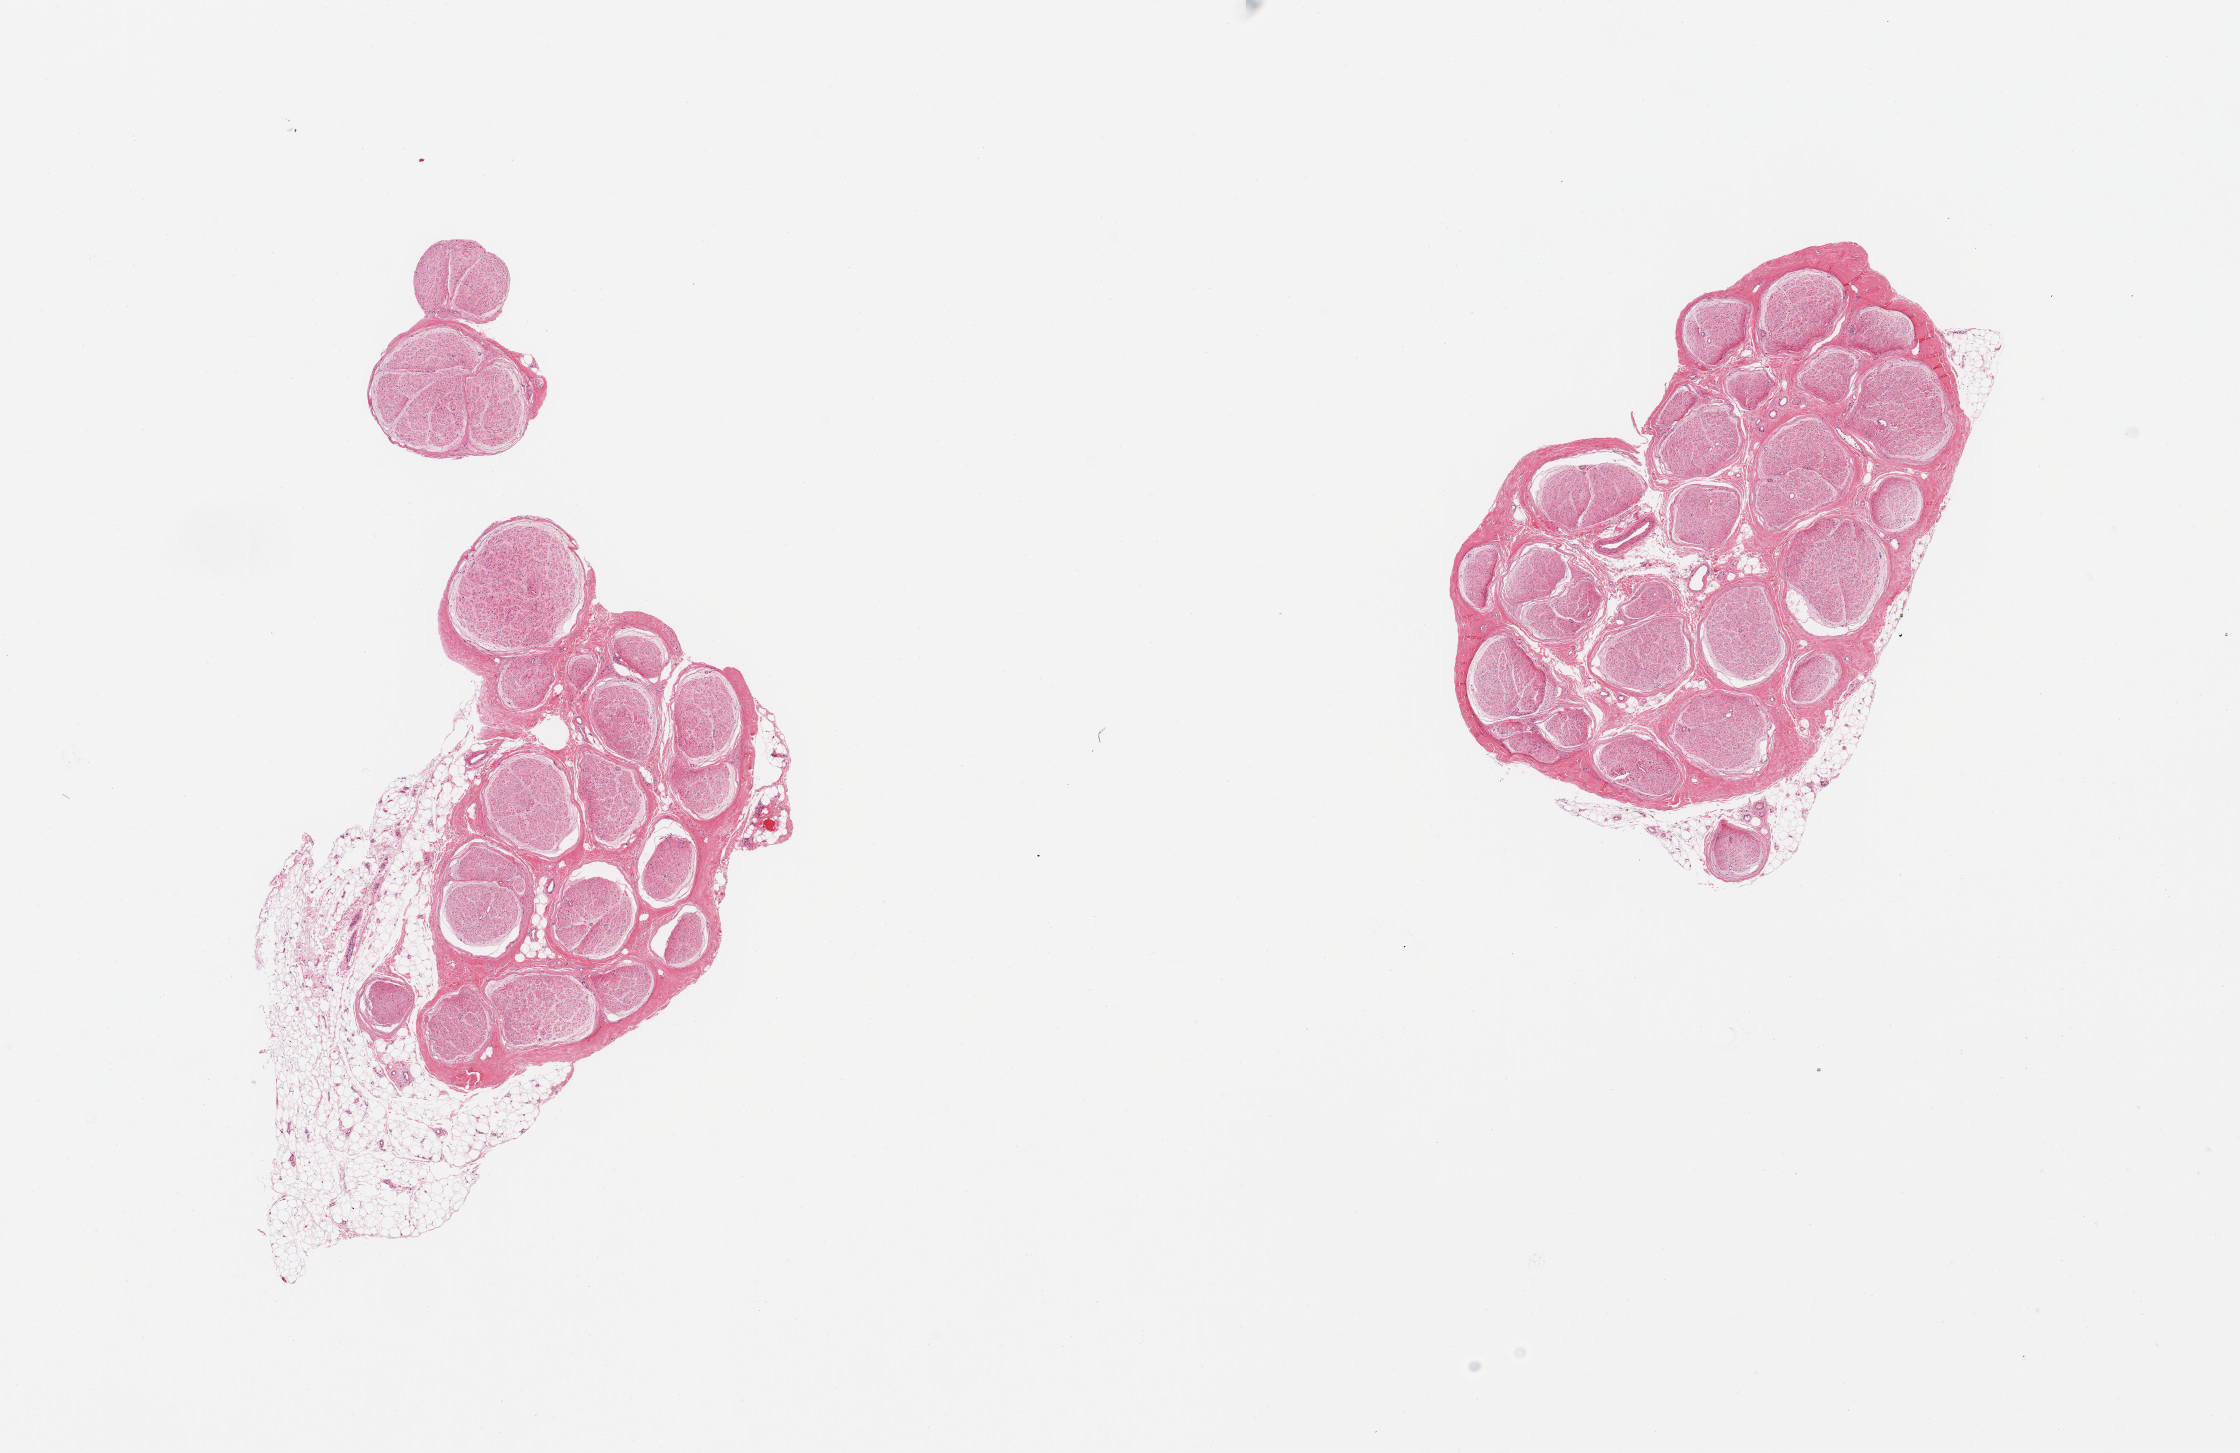
Digitized hematoxylin and eosin (H&E)-stained section, brightfield, low-resolution overview of the scanned area, about 17.7 x 11.5 mm (acquisition: 20x scan). PAXgene-fixed paraffin-embedded (PFPE) section. Section of tibial nerve (target tissue). Donor tissue sample.
Pathologist's review note for this sample: 2 pieces, ~2mm nubbin of adherent fat.